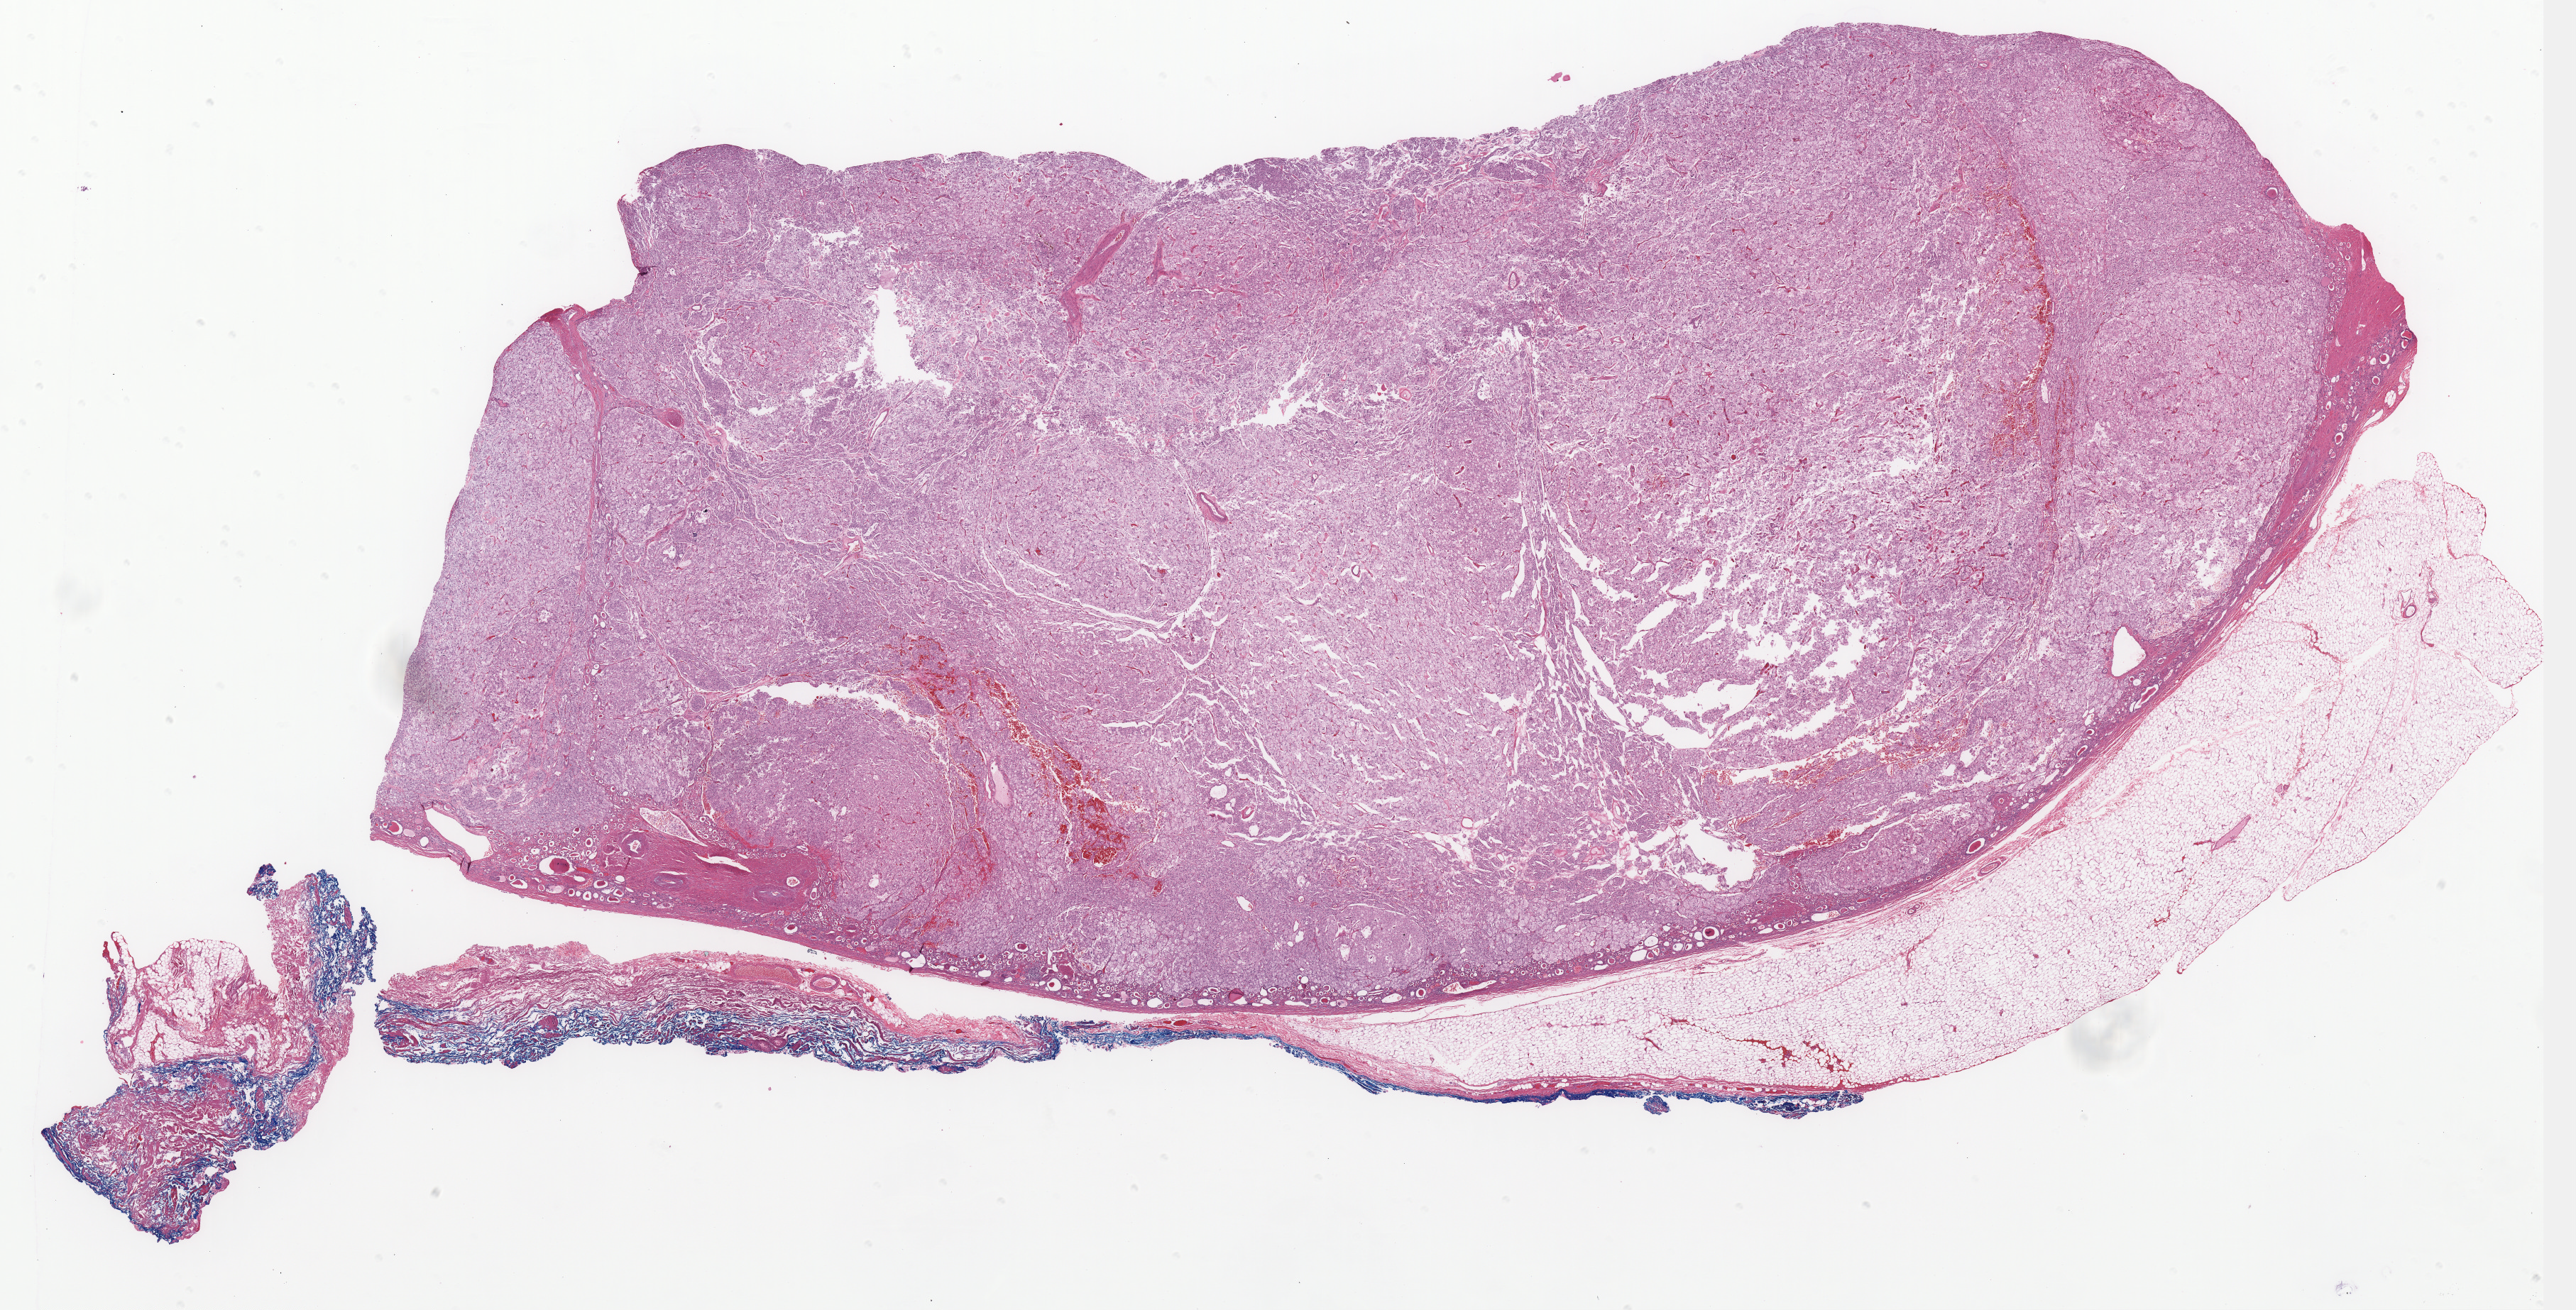
Whole-slide histology image, H&E-stained, shown as a low-resolution overview of the whole scanned area (about 29.0 x 14.8 mm); formalin-fixed paraffin-embedded (FFPE) diagnostic section; kidney, primary tumour sample. Male, age 62 years at initial diagnosis.
• AJCC pathologic stage: II
• lymph nodes positive (case pathology): 0 of 1 examined
• histologic diagnosis: Renal cell carcinoma, chromophobe type